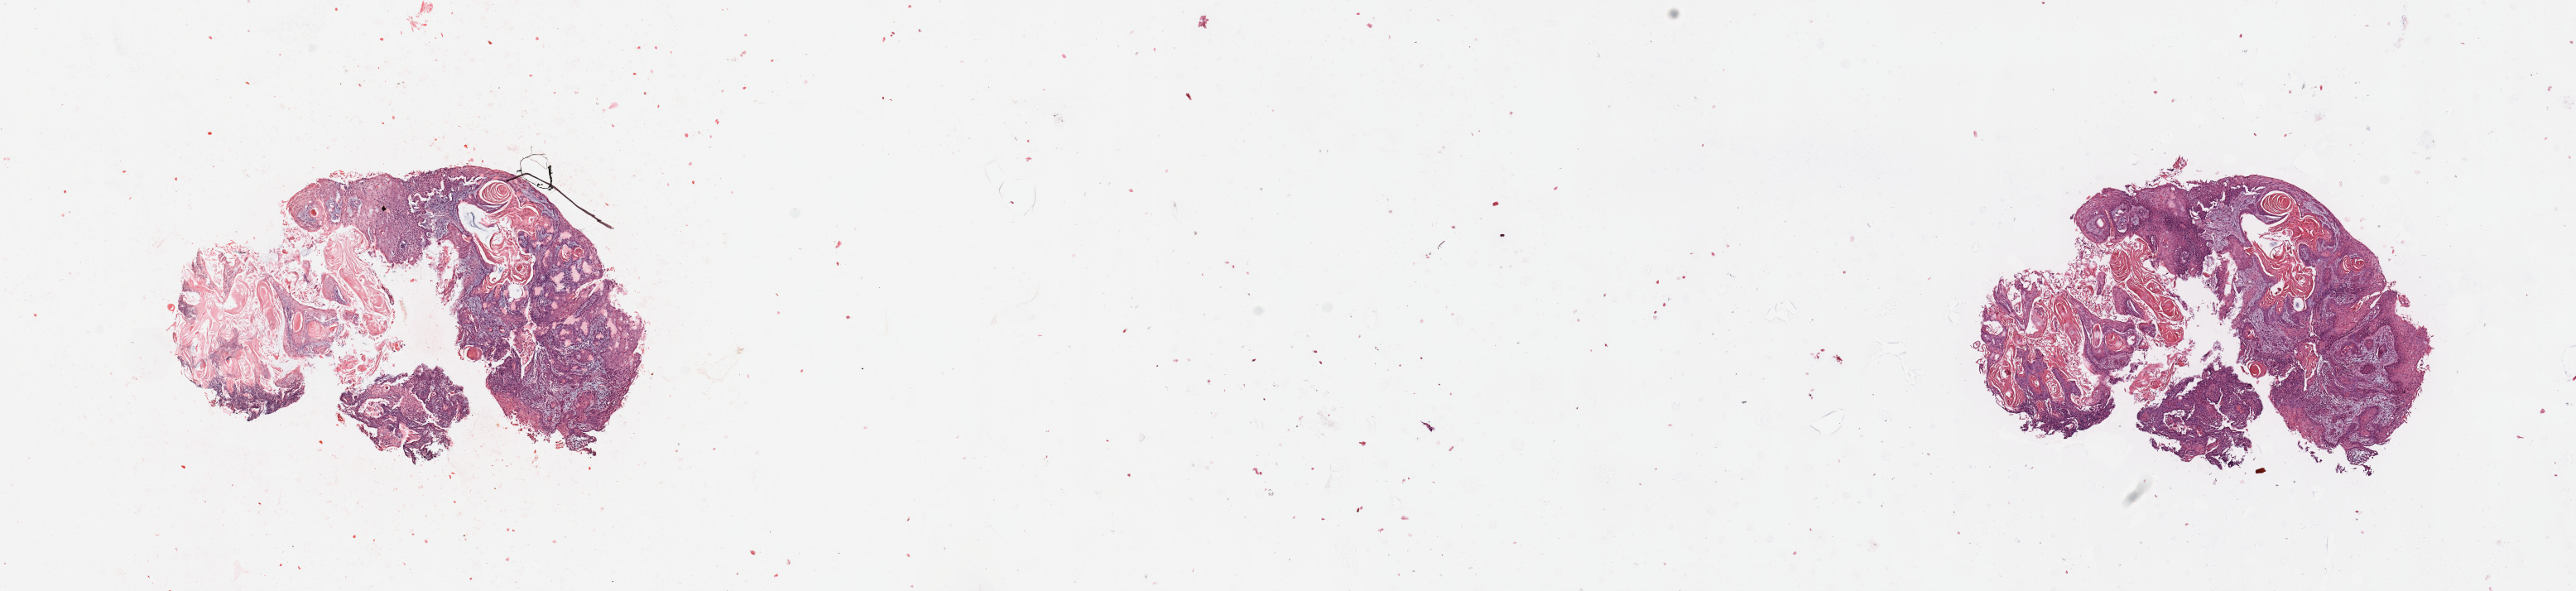
Digitized H&E tissue section (whole slide), whole scanned area (about 24.6 x 5.6 mm) shown as a low-resolution overview; tumour tissue sample, sampled site: larynx. 72-year-old male patient. Histologic grade: G2 (moderately differentiated). Pathologist review of this section (percent, as recorded): tumour nuclei 85%, necrosis 2%.
AJCC pathologic stage: IVA. Primary tumour site (as recorded): larynx. Histologic diagnosis: Squamous cell carcinoma, NOS.